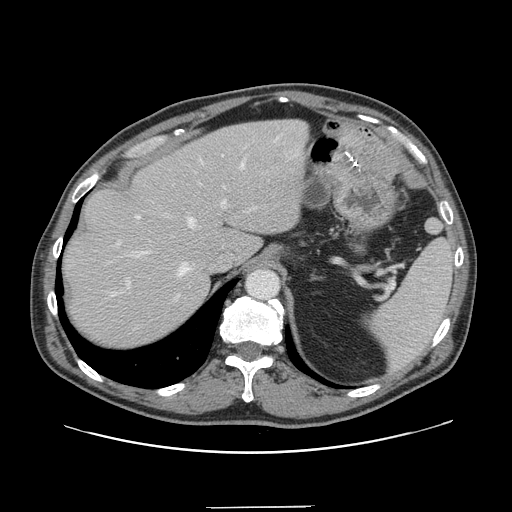
Contrast-enhanced abdominal CT, one axial slice. Position 111 of 139 along the scan axis. 120 kVp. Intravenous contrast given. Soft-tissue window (W 400 / L 40 HU). 2.5 mm slice thickness. 512 × 512 image matrix, field of view 397 × 397 mm. Male patient, age 64 years. Case-level facts recorded for this patient, not image findings: diagnosis: colorectal cancer liver metastases, imaged before liver resection; multiple liver metastases: yes; largest metastasis: 3.5 cm.
Structures marked on this image (outlined manually by an expert reader):
- hepatic veins: bounding box <132,160,245,300> (left, top, right, bottom; pixels)
- liver: <63,121,308,347>
- planned liver remnant (the part of the liver to remain after resection): <63,122,270,347>
- portal vein (with intrahepatic branches): <117,155,254,289>